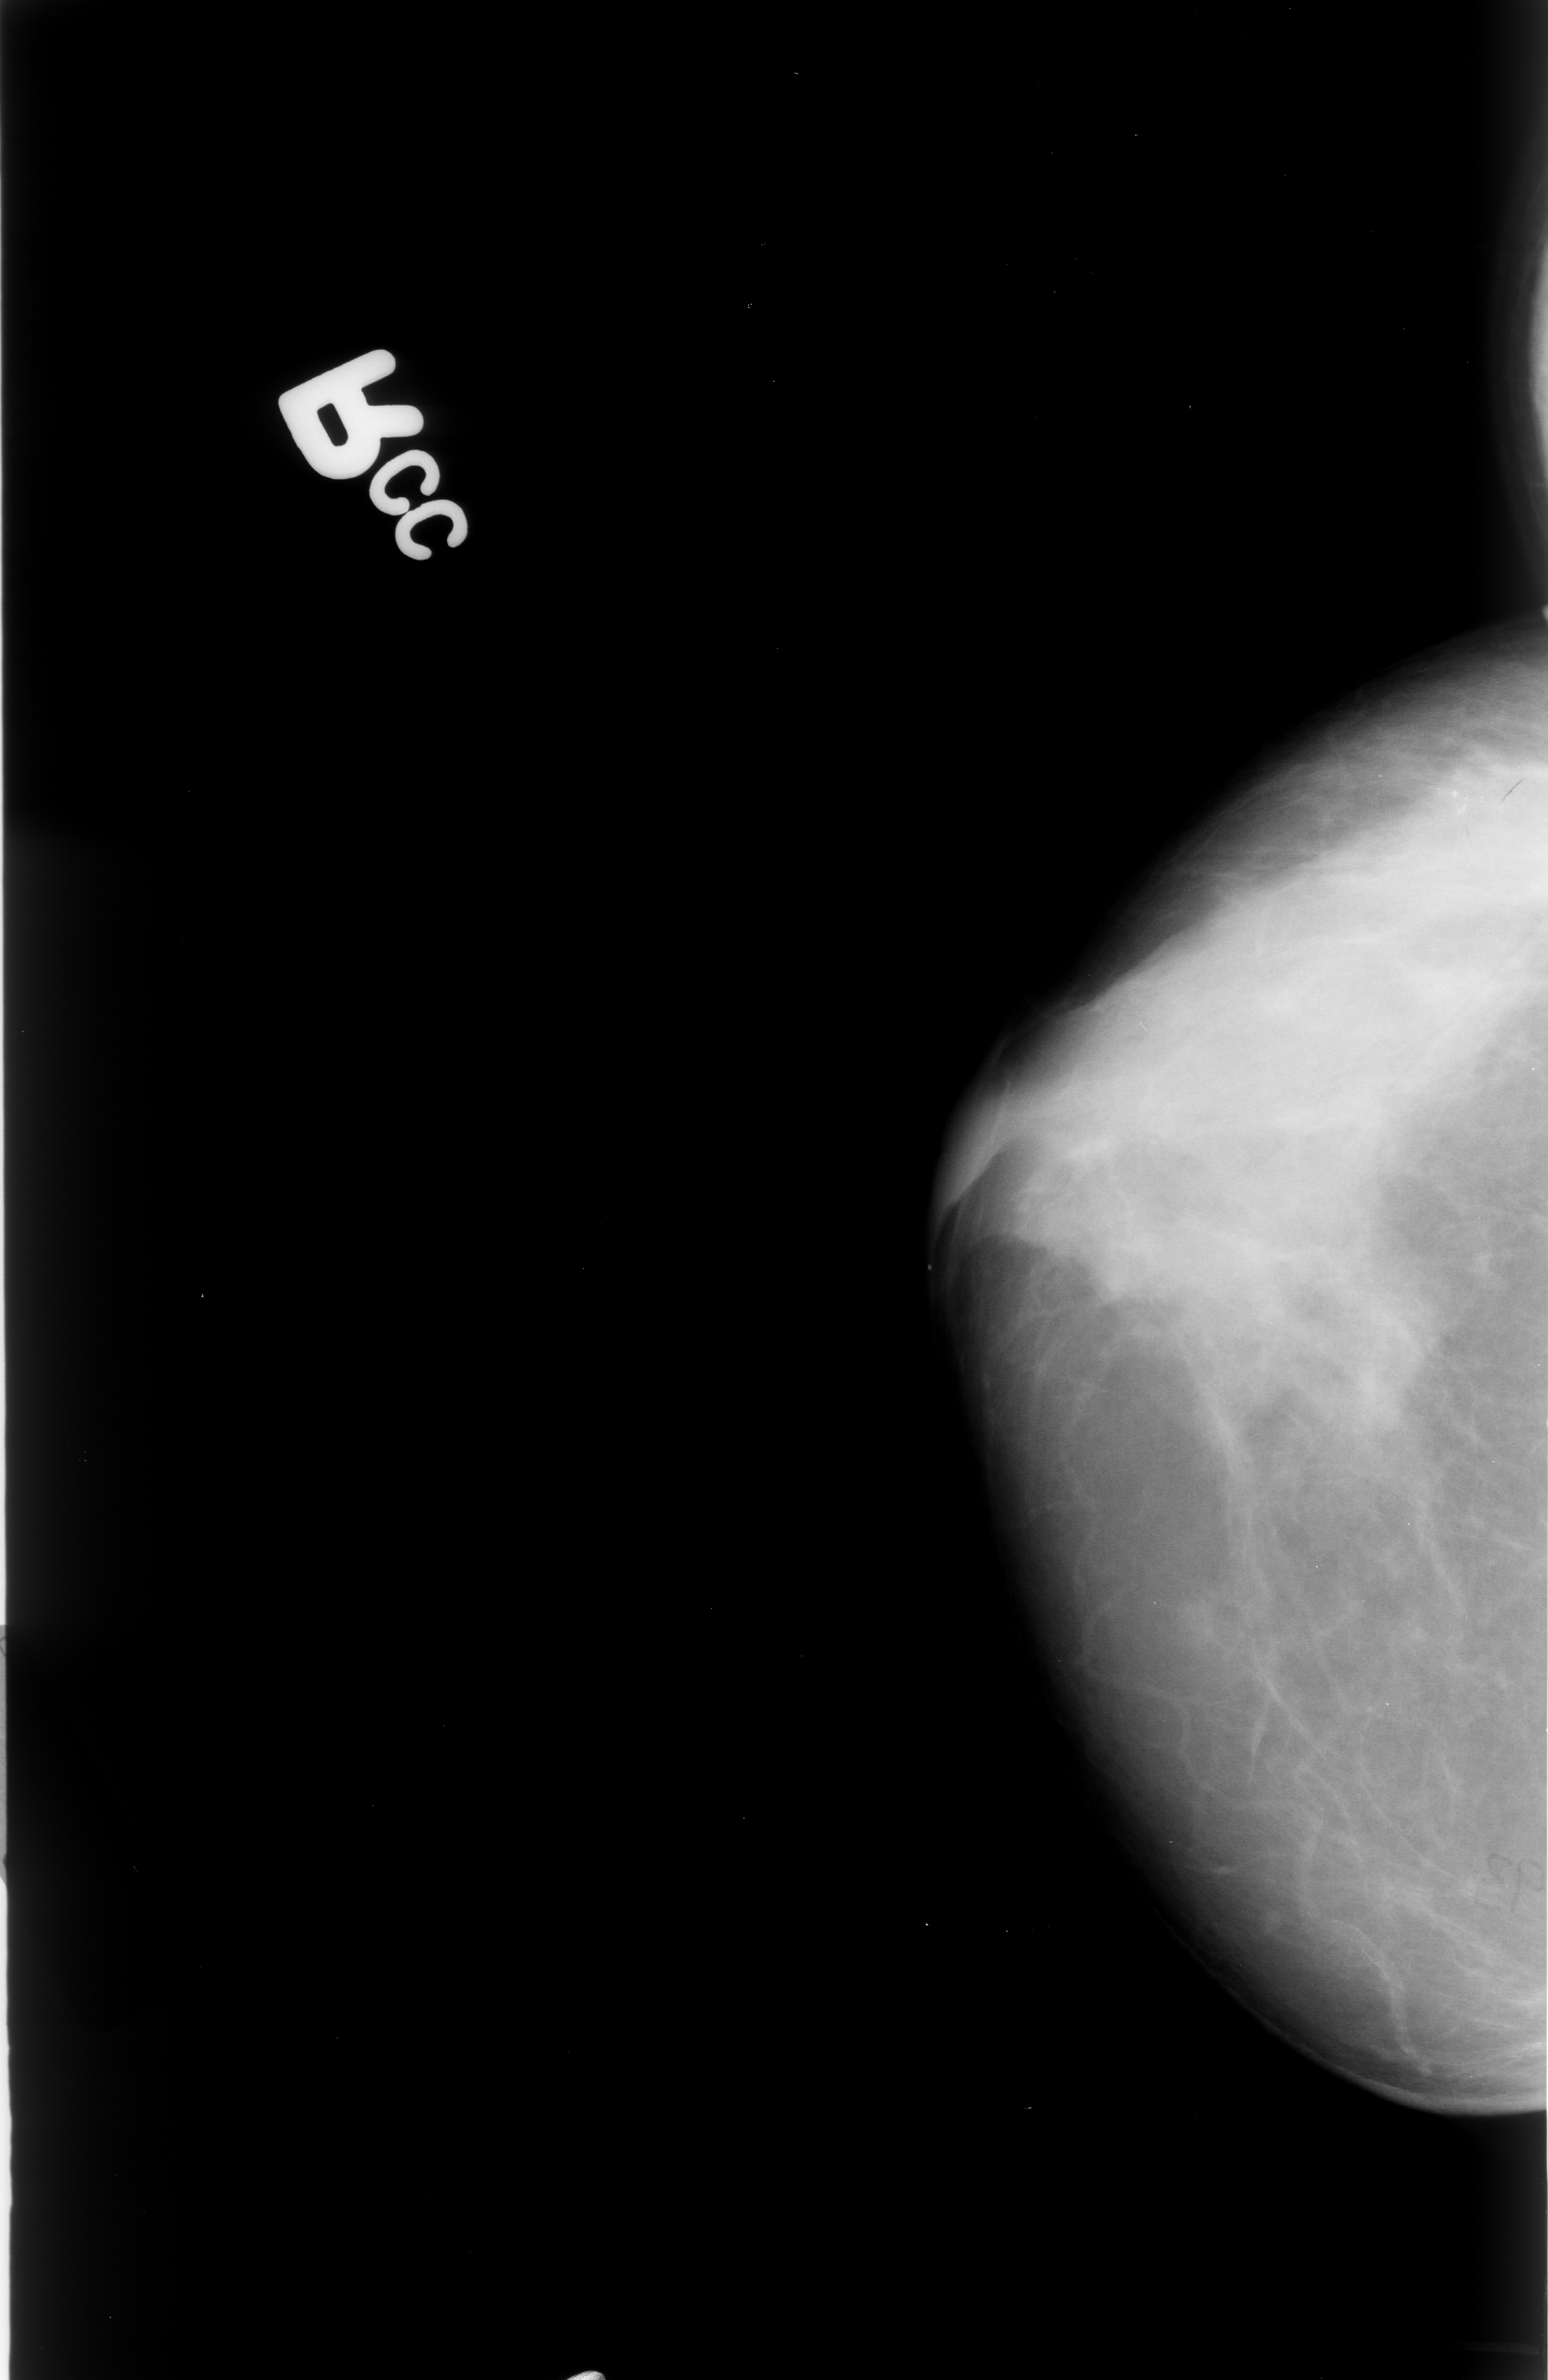
Digitized screen-film mammogram. Right breast. Craniocaudal (CC) view. BI-RADS breast density category 3 (scale 1–4). 1548 × 2380 image matrix.
Expert-marked regions of interest on this film, with their recorded descriptors:
- calcifications, morphology pleomorphic, distribution clustered; BI-RADS assessment category 4; pathology (as recorded): malignant: bounding box (x1, y1, x2, y2) in pixels: (1425, 742, 1532, 850)